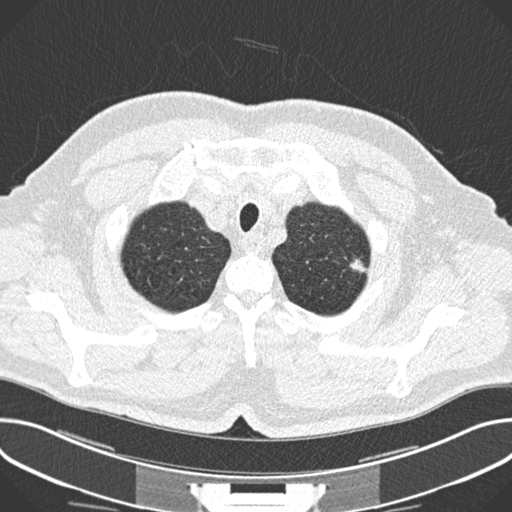
Low-dose screening chest CT, one axial slice; position 218 of 244 along the scan axis; reconstruction kernel B30f; 120 kVp; lung window (W 1500 / L -600 HU); 2 mm slice thickness; 512 × 512 image matrix, field of view 380 × 380 mm.
Outlined on this slice (outlined manually by an expert reader):
- lesion 1 (tumor, upper lobe of left lung): bounding box <349,259,367,273> (left, top, right, bottom; pixels)